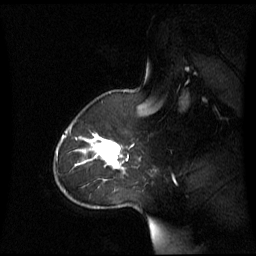
Breast MRI (dynamic contrast-enhanced), one sagittal slice. Position 47 of 60 along the scan axis. Dynamic contrast-enhanced series, image 2 of 3 at this slice position (ordered by acquisition). 1.5 T. TE 4.2 ms, TR 8.4 ms. 2.8 mm slice thickness. 256 × 256 image matrix. Female patient, age 43 years. Case-level facts recorded for this patient, not image findings: setting: breast cancer imaged before/during neoadjuvant chemotherapy; receptor status: triple-negative.
Outlined on this slice (semi-automatically segmented with operator editing):
- analysis volume of interest (the breast-tissue region the enhancement analysis was run in; not a lesion): bounding box <62,124,125,180> (left, top, right, bottom; pixels)
- tumour enhancement mask (voxels above the 70 % enhancement threshold inside the analysis volume of interest): <75,134,124,169>